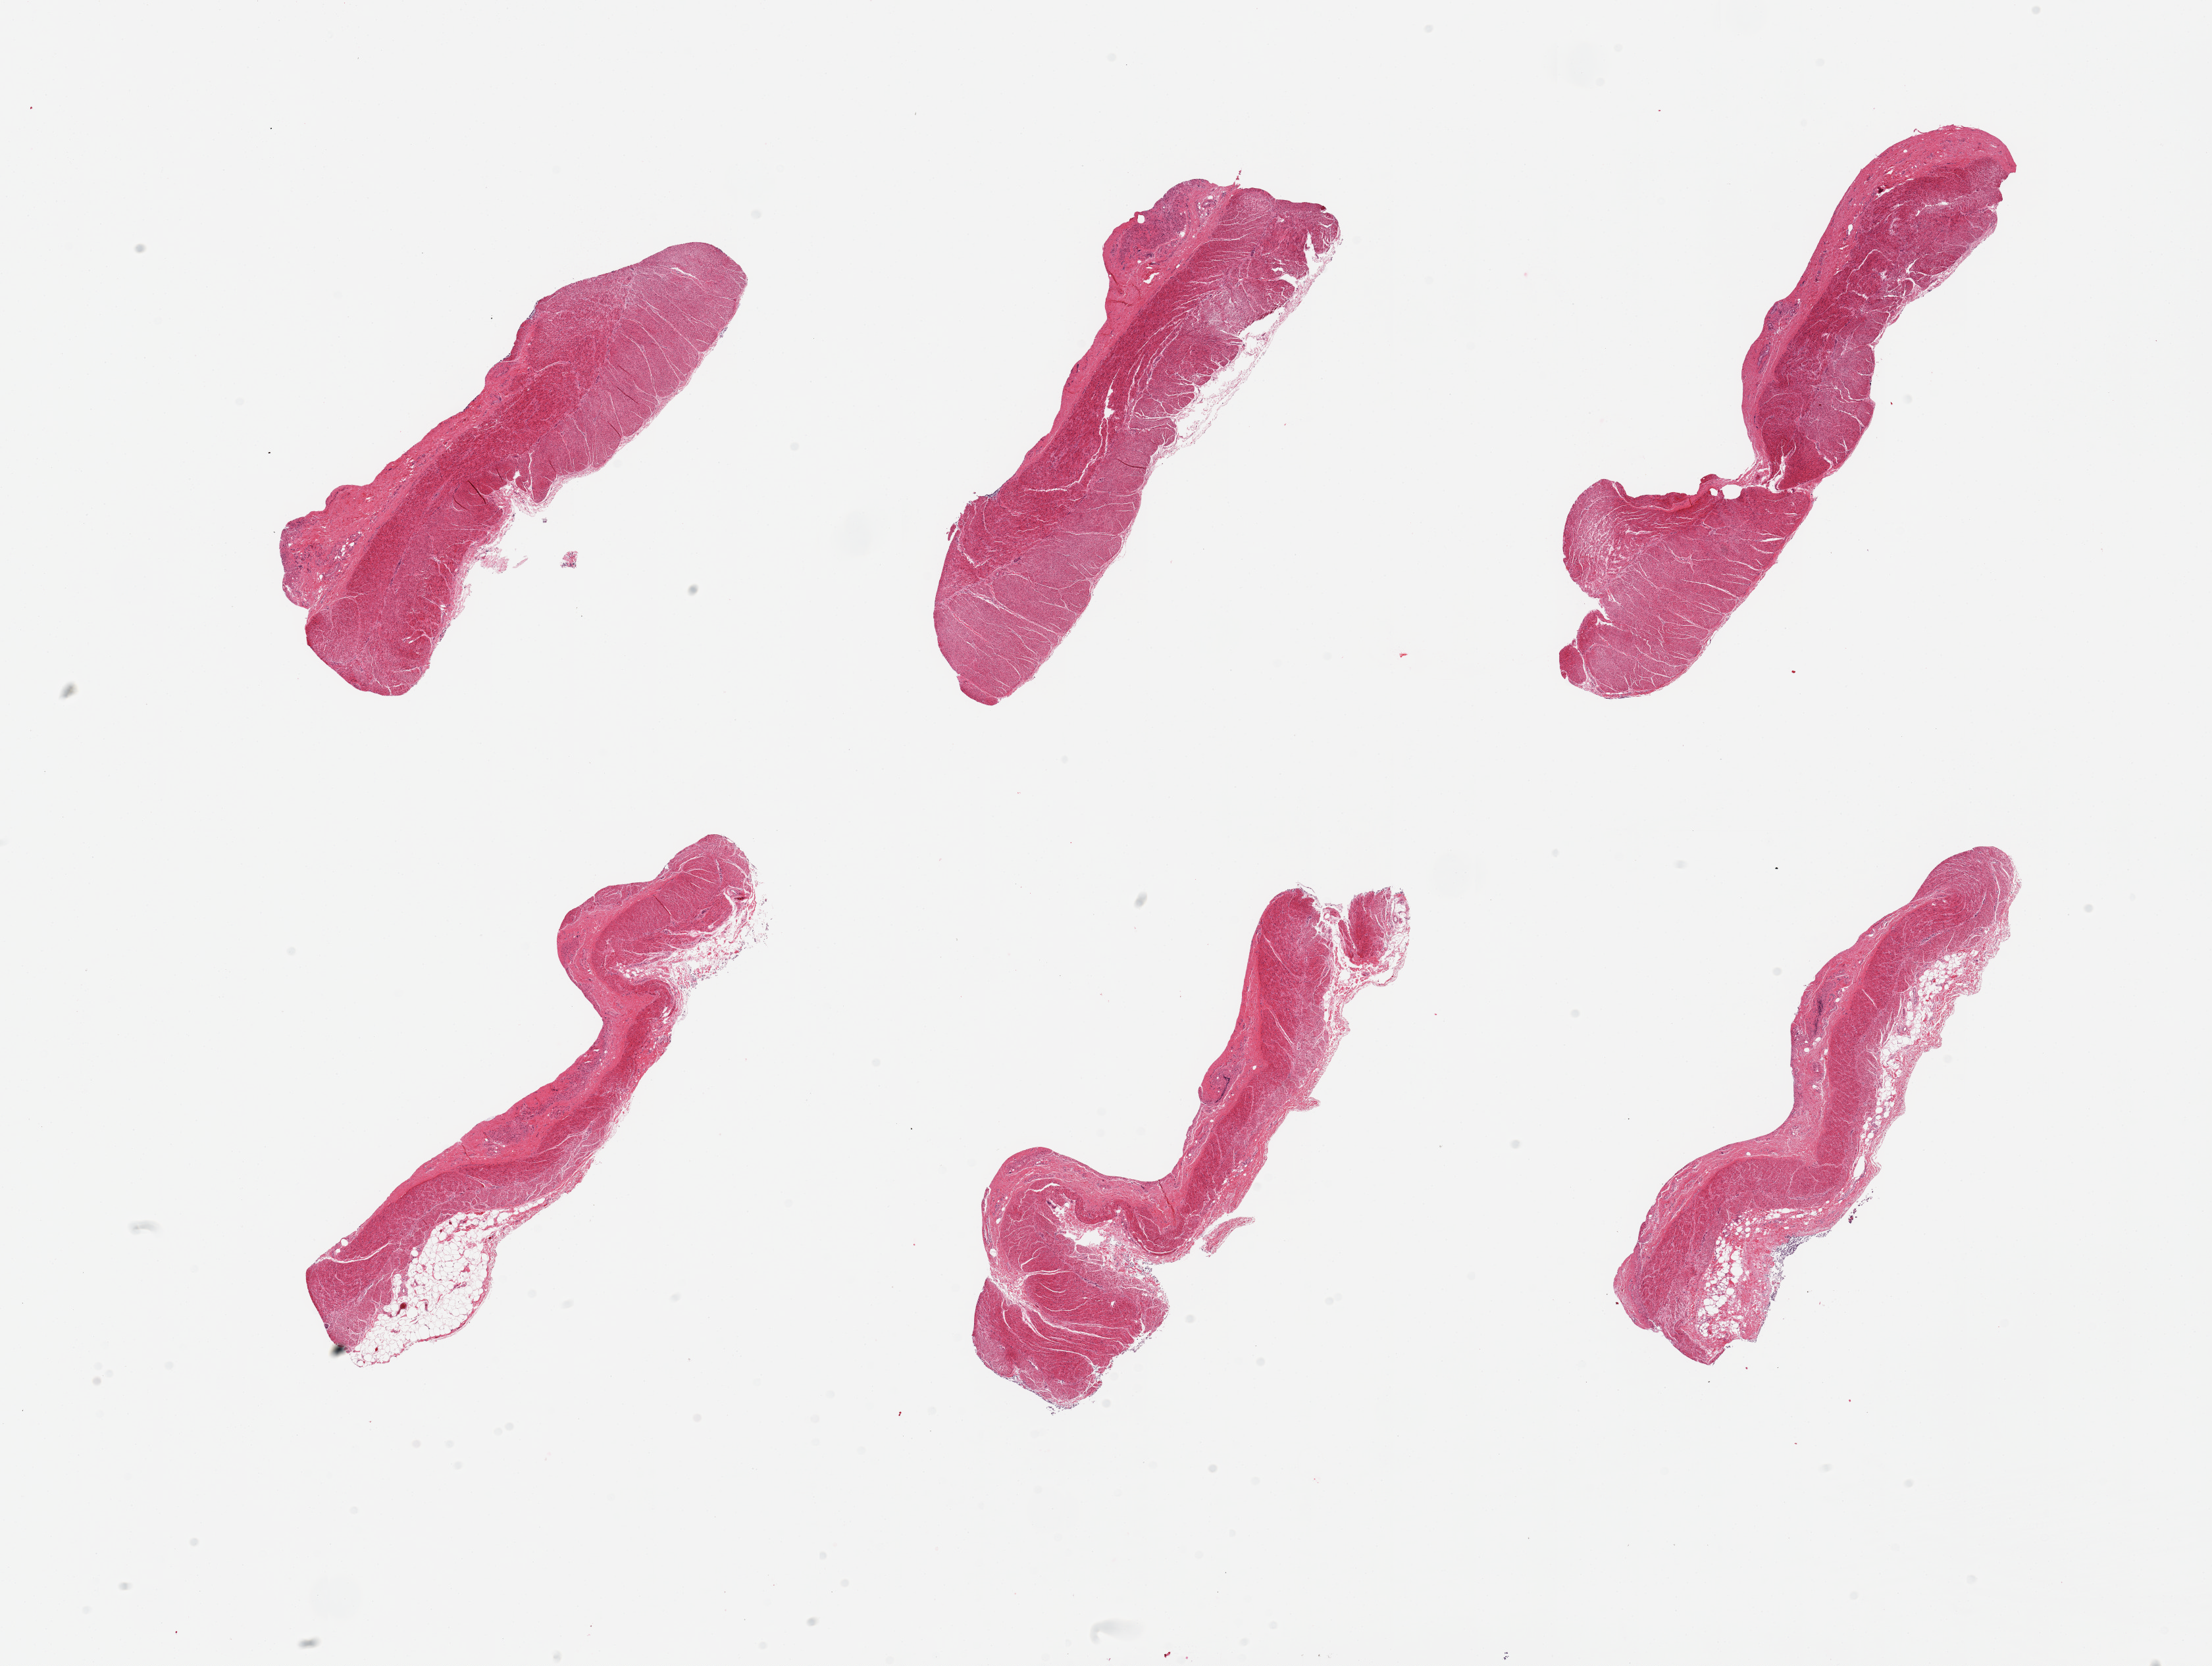
Haematoxylin and eosin whole-slide image — whole scanned area (about 26.6 x 20.0 mm) shown as a low-resolution overview. PAXgene-fixed paraffin-embedded (PFPE) section. Section of sigmoid colon (target tissue). Donor tissue sample. Donor sex: male.
Pathologist's review note for this sample: 6 pieces, all muscularis.